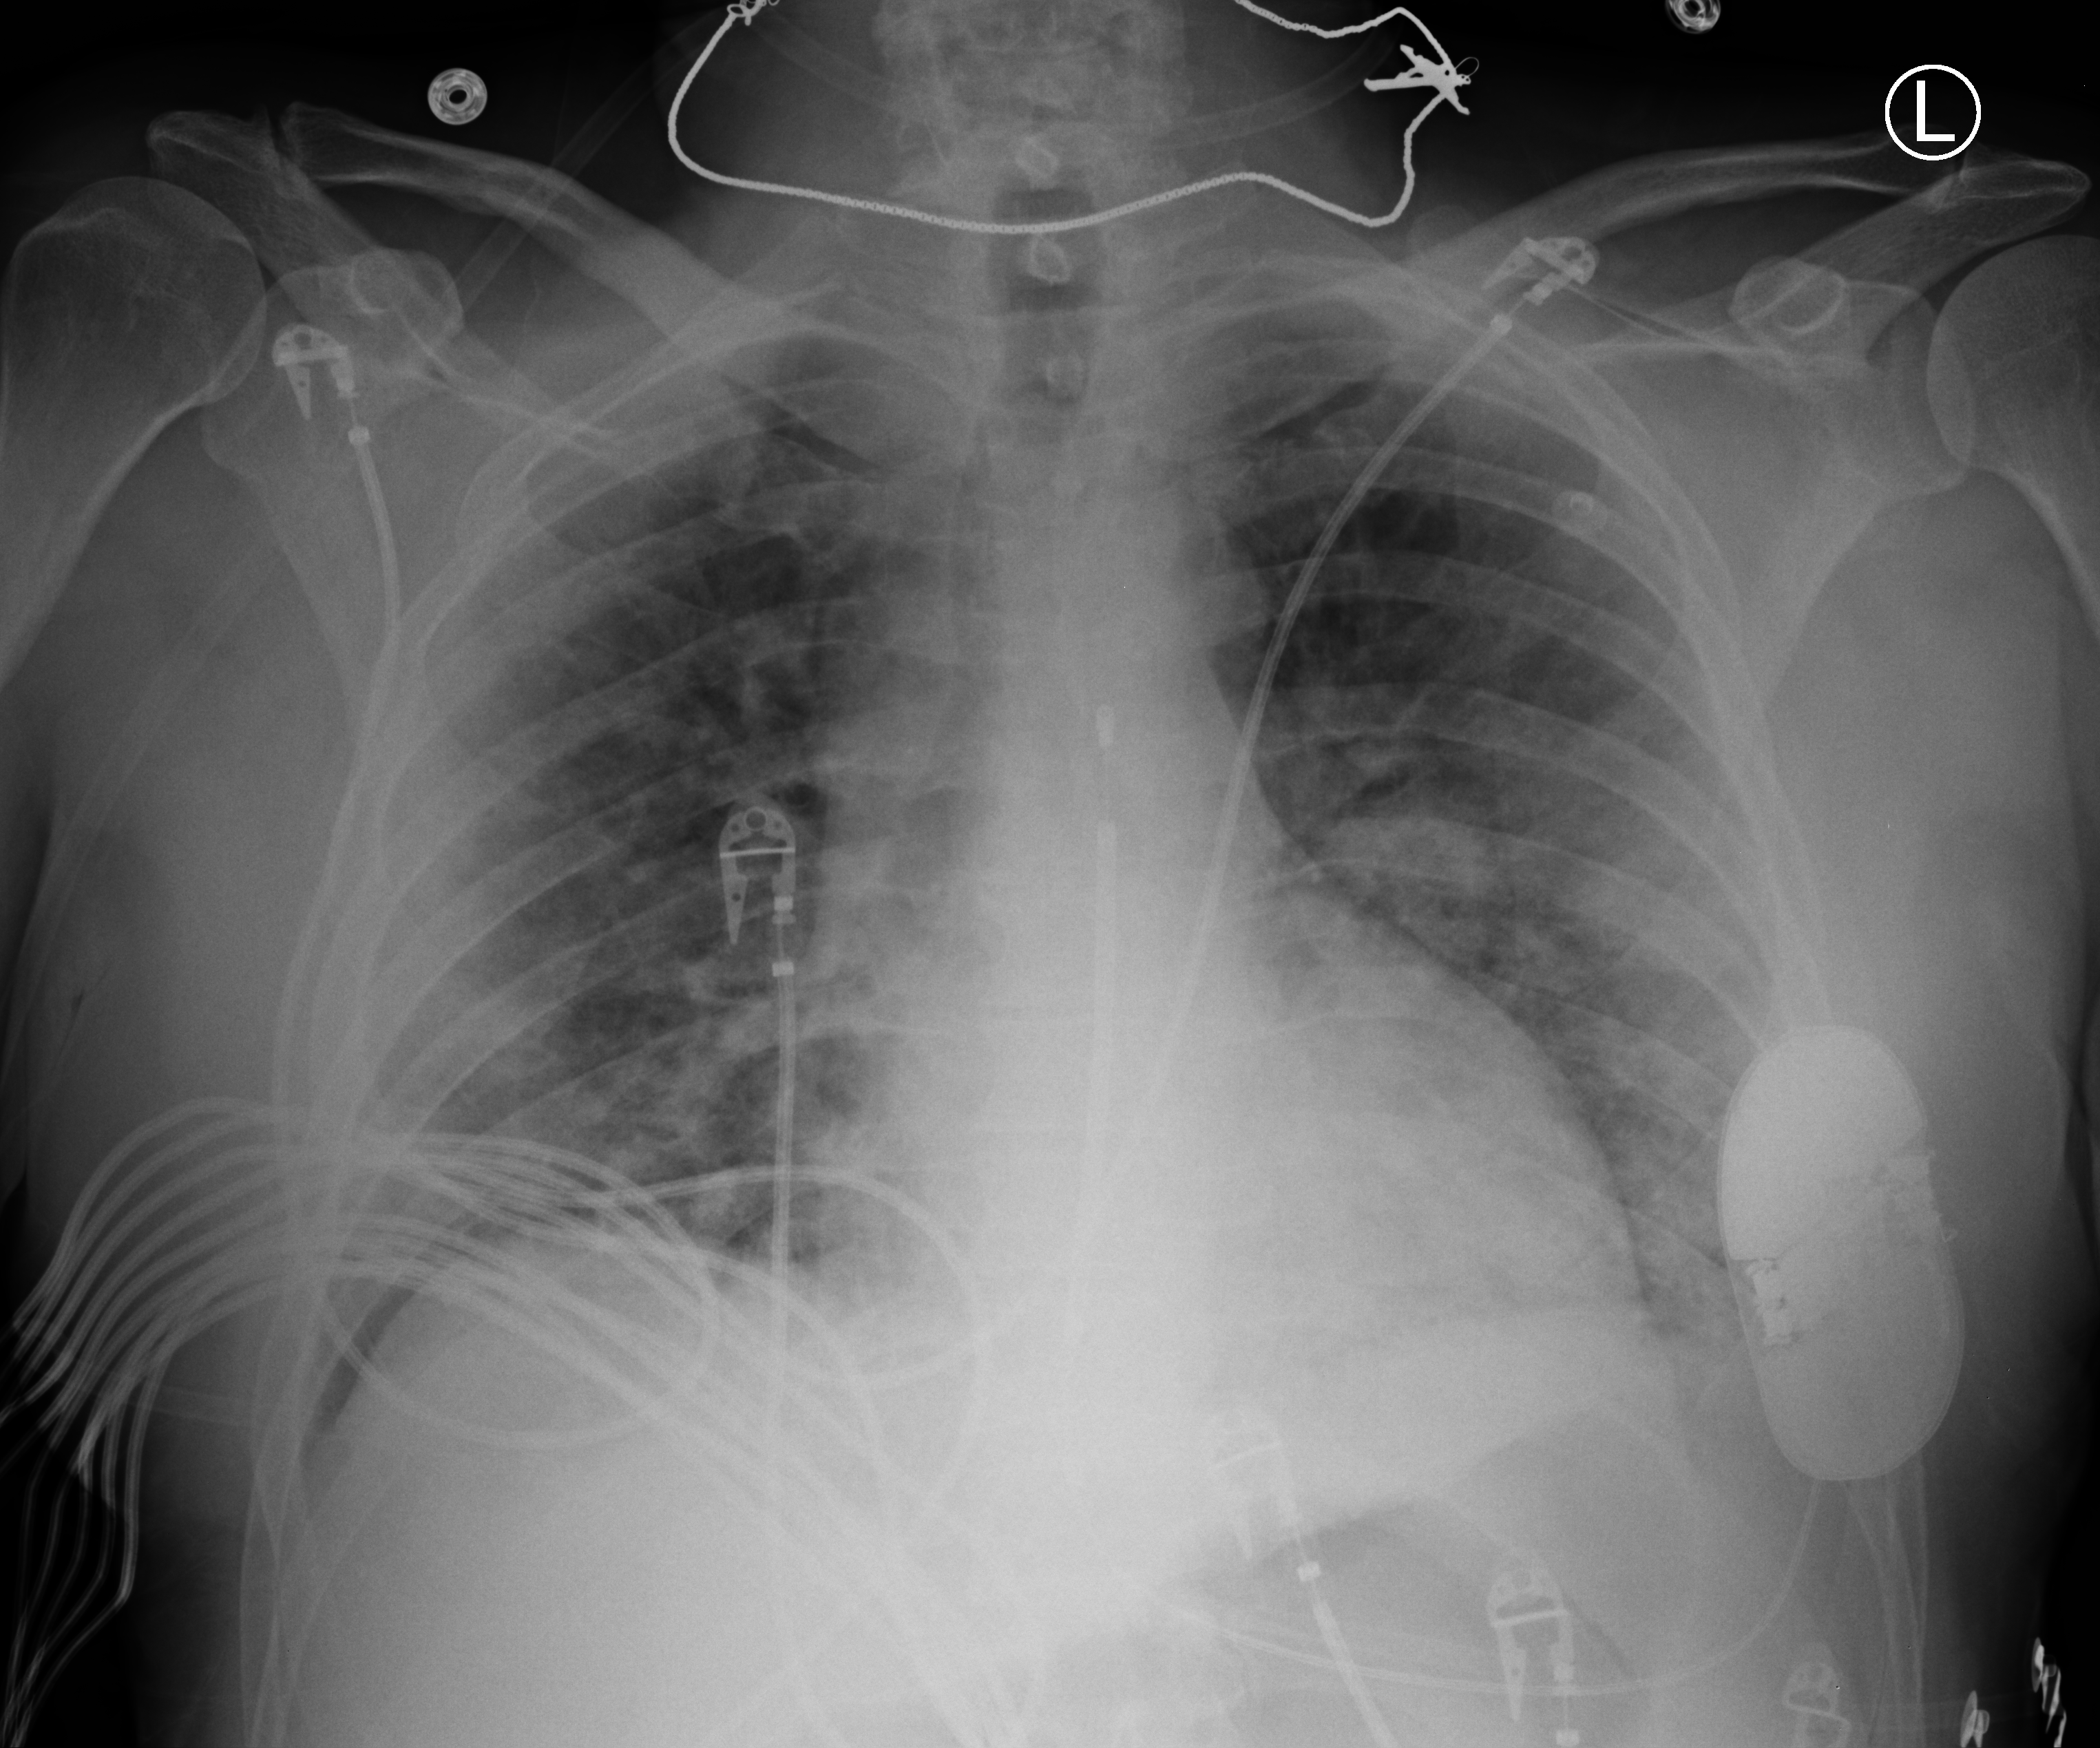
Bedside chest radiograph (computed radiography); anteroposterior (AP) projection. Male patient hospitalised with COVID-19, age 18–59 years.
Admission-level facts for this patient (not findings on this image; timing relative to this image not recorded):
- length of hospital stay: 19 days